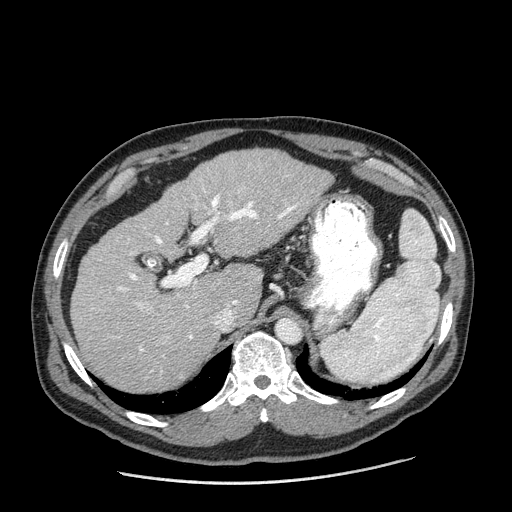
Contrast-enhanced abdominal CT (liver protocol), one axial slice; 120 kVp; one of 2 acquisitions stored at this slice position; soft-tissue window (W 400 / L 40 HU); 2.5 mm slice thickness; 512 × 512 image matrix, field of view 400 × 400 mm. From the clinical record (not read from this slice): diagnosis: hepatocellular carcinoma (patient treated with transarterial chemoembolisation; whether this scan precedes or follows treatment is not stated here); TNM stage (as recorded): Stage-II; Child-Pugh class: A; tumour differentiation: moderately differentiated; tumour size: 2.6 cm.
Outlined on this slice (semi-automatically segmented with operator editing):
- liver parenchyma outside the tumour (the mass and vessels are separate outlines, so this box may not span the whole liver): box from (x=70, y=149) to (x=332, y=392) px
- liver vessels: (x=117, y=195)–(x=297, y=352)